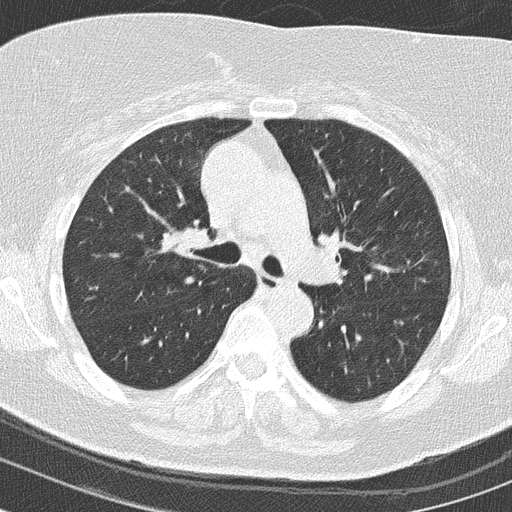
Axial slice from a low-dose chest CT screening exam; baseline annual screen; lung window (W 1500 / L -600 HU); slice 50 of 149 in the series; 512 × 512 image matrix, field of view 294 × 294 mm. Female, age 63 years at enrolment. Former smoker at enrolment.
Lesion marked by an expert reader, box from (x=155, y=217) to (x=225, y=269) px. No non-calcified nodule or mass ≥4 mm was recorded by the screening reader at this exam. Participant outcome: lung cancer diagnosed 149 days after this screen — squamous cell carcinoma, keratinizing, NOS, right upper lobe, moderately differentiated (G2), stage IIA (AJCC 6th edition), 42 mm at pathology.